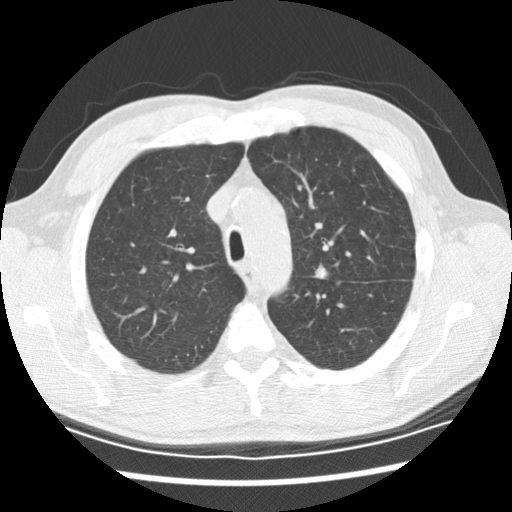
Low-dose screening chest CT, axial slice, second screening round (one year after baseline), lung window (W 1500 / L -600 HU), standard (soft-tissue) reconstruction kernel (STANDARD), 120 kVp, 512 × 512 image matrix, field of view 340 × 340 mm. Male, age 59 years at enrolment. Current smoker at enrolment.
- Lesion marked by an expert reader, bounding box [x1, y1, x2, y2] px = [304, 260, 340, 293].
- Reader record for this screening exam (exam-level; its link to the box is not recorded): non-calcified nodule or mass ≥4 mm, left upper lobe, 8 × 7 mm, spiculated (stellate) margins, soft tissue attenuation, pre-existing on the prior screen: yes; interval growth: yes.
- Official screen result: positive, change unspecified: nodule(s) >= 4 mm or enlarging nodule(s), mass(es), or other non-specific abnormalities suspicious for lung cancer.
- Later outcome: lung cancer diagnosed 251 days after this screen — adenocarcinoma, NOS, left upper lobe, left lower lobe, poorly differentiated (G3), stage IV (AJCC 6th edition).